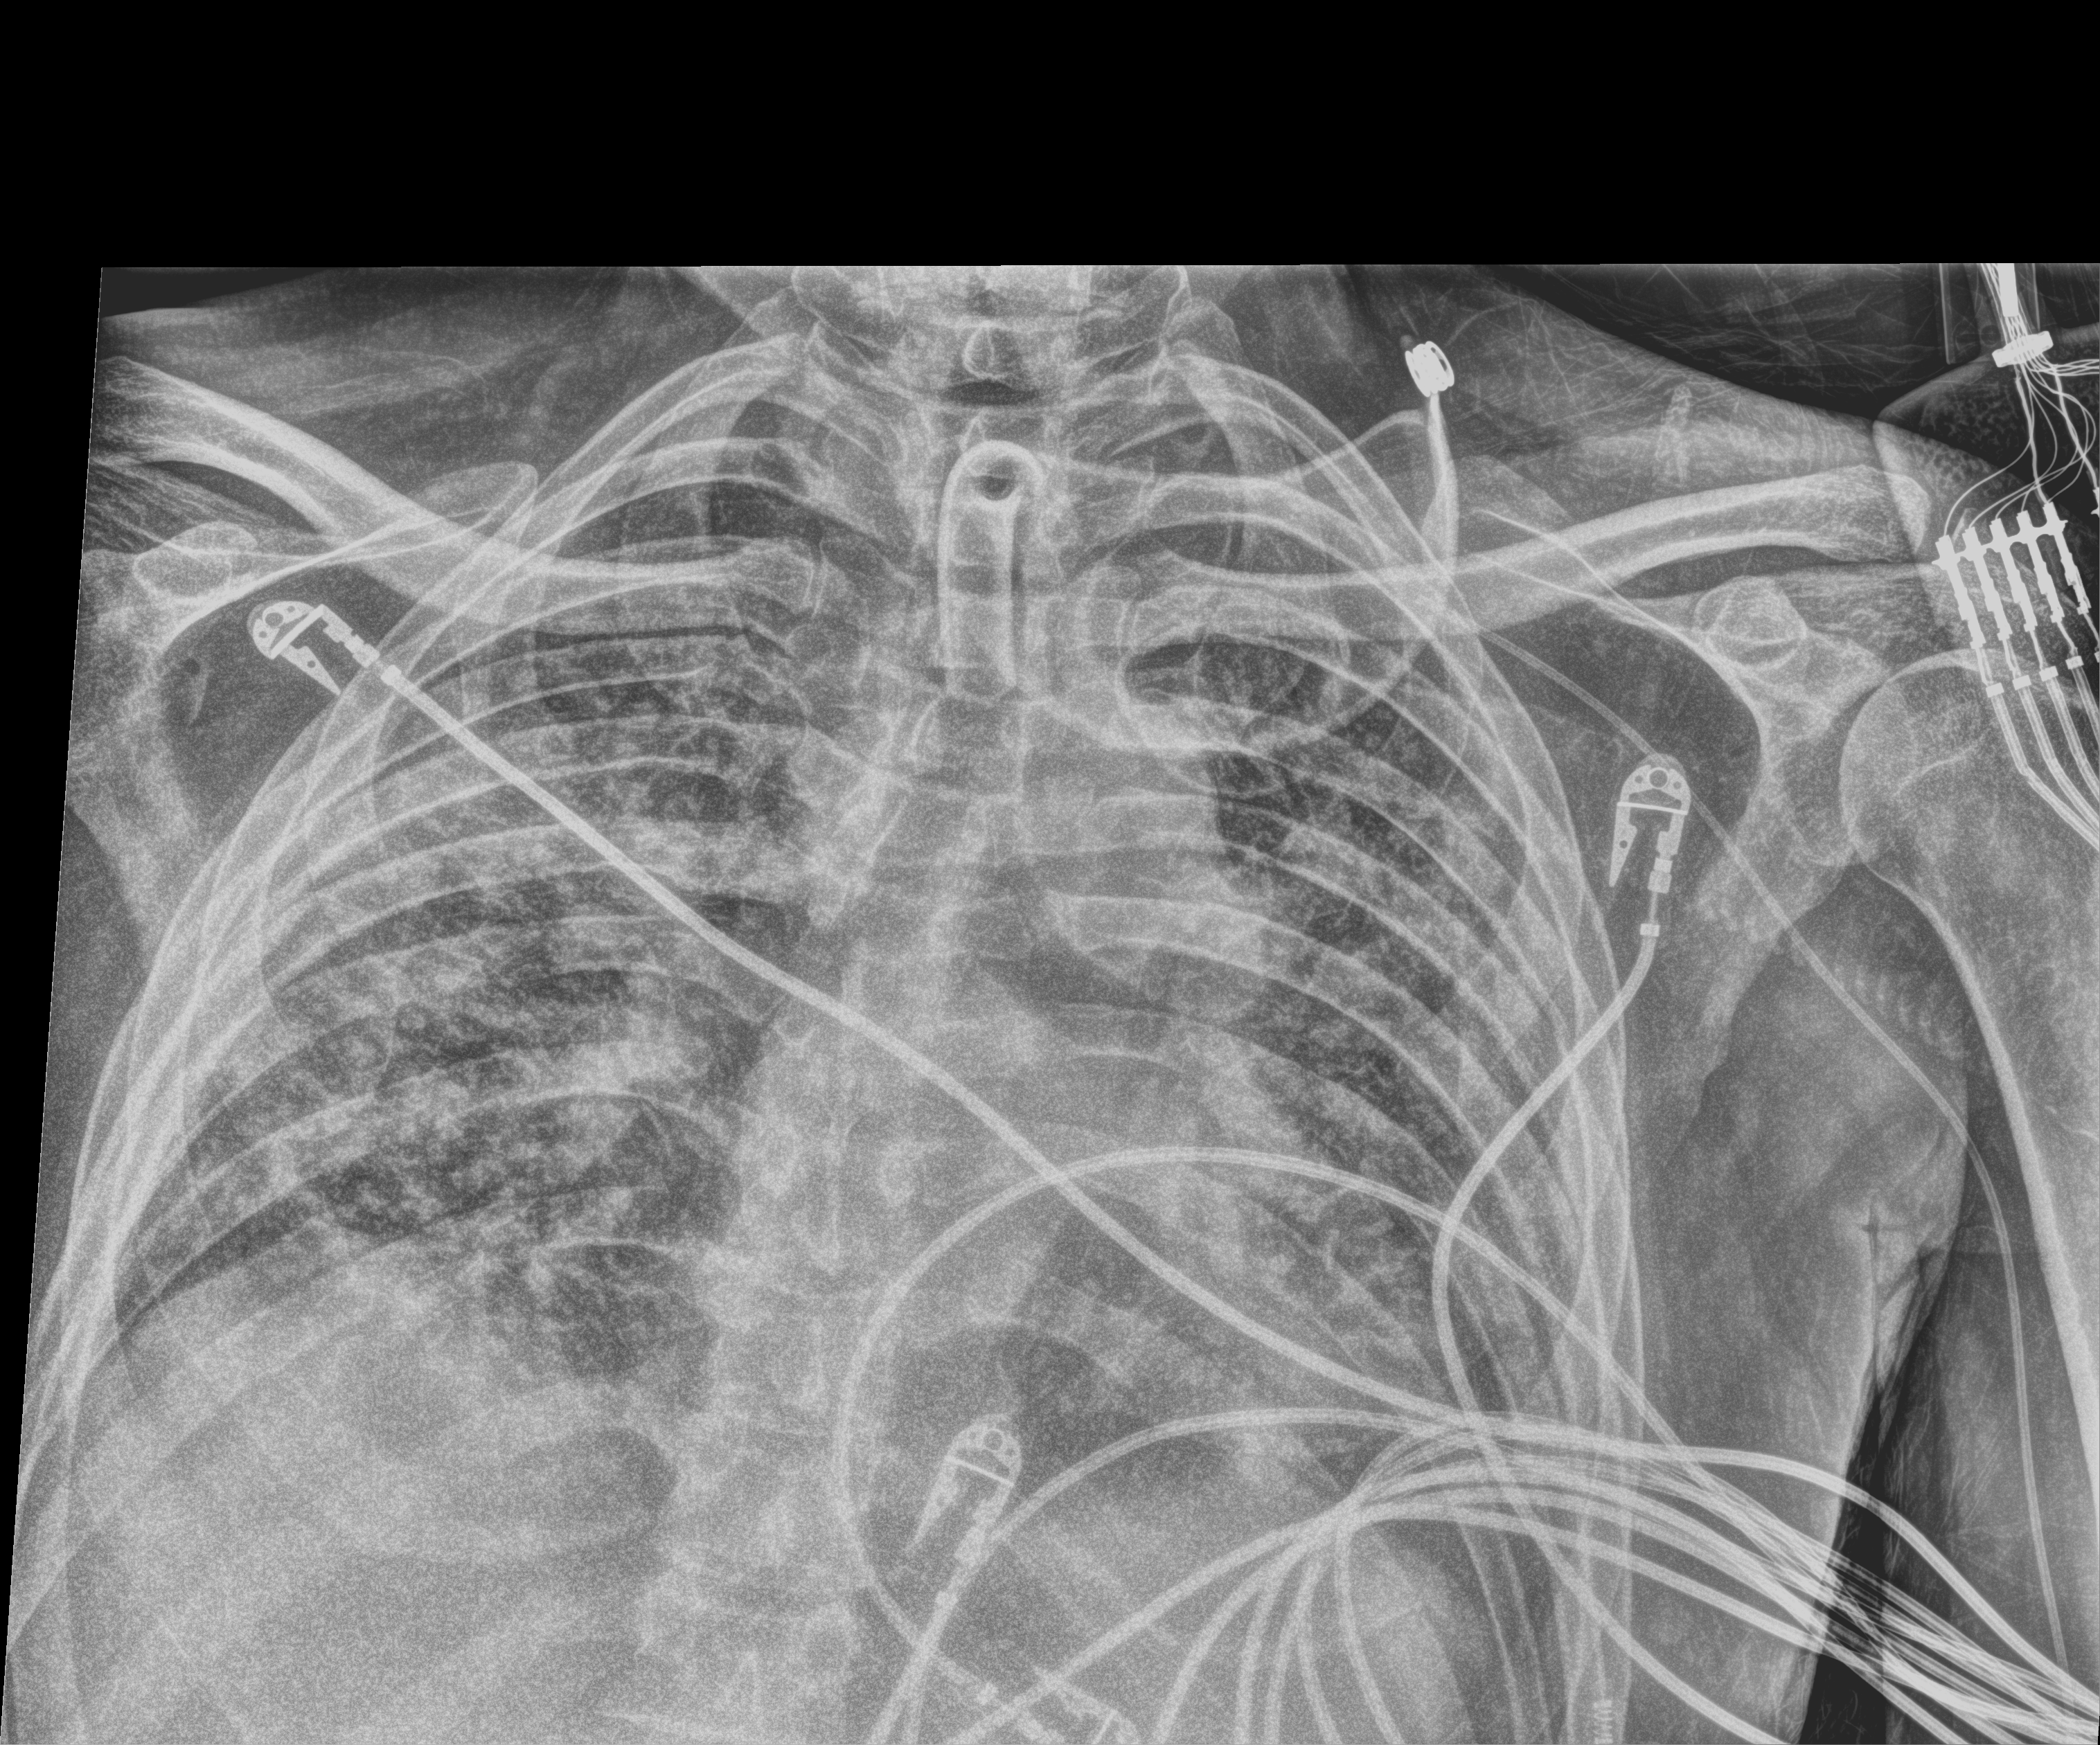
Bedside chest radiograph (digital radiography). Patient hospitalised with COVID-19; male, aged 18–59 years.
From the hospital-stay record, not from the radiograph (when in the stay this image was taken is not recorded): mechanically ventilated during this hospital stay: yes; admitted to intensive care during this hospital stay: yes.